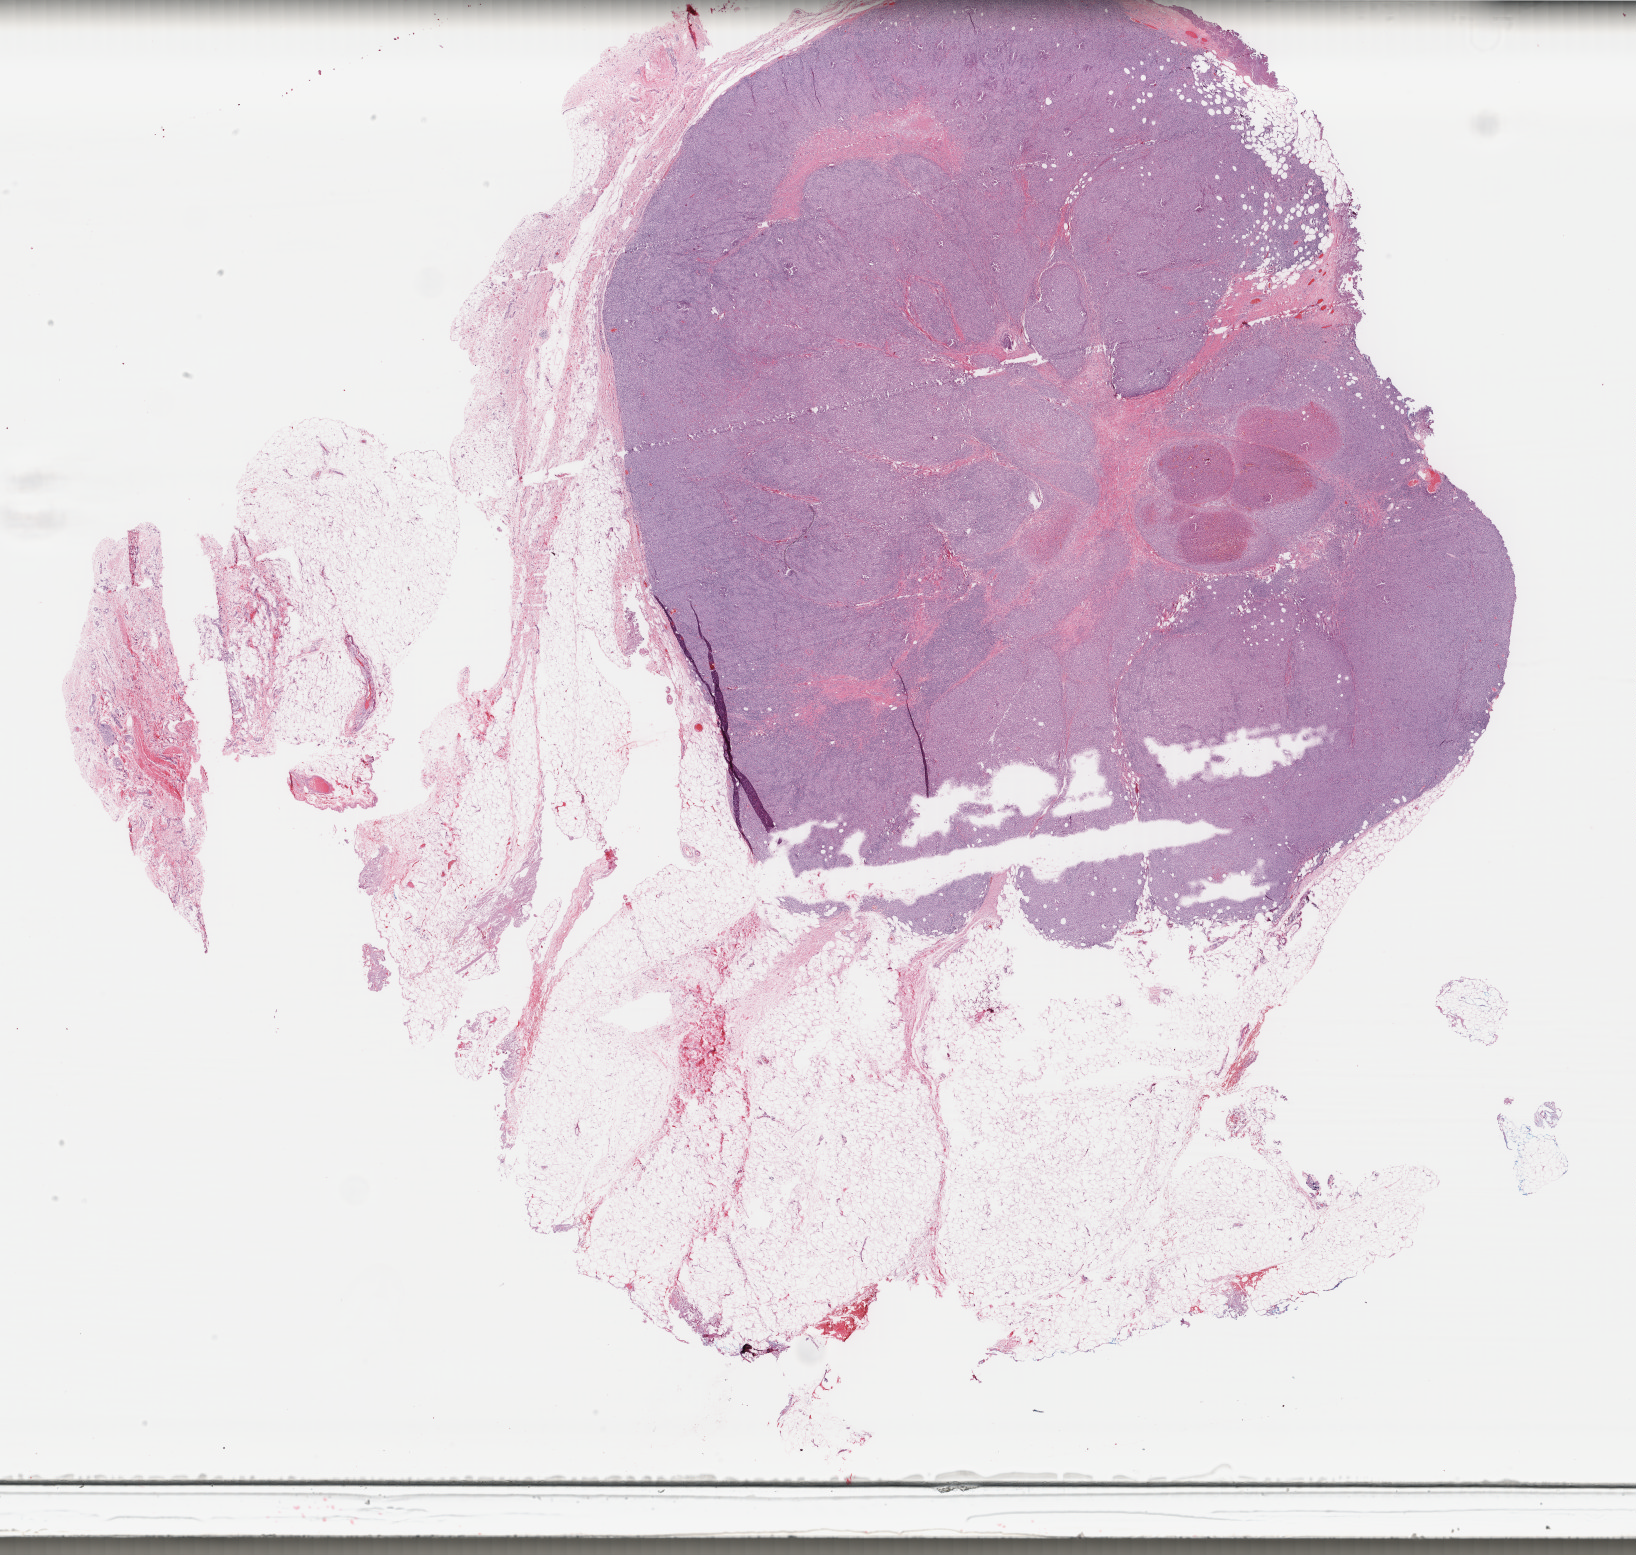
Hematoxylin and eosin (H&E) stained whole-slide image, whole scanned area (about 26.0 x 24.7 mm, acquisition: 40x scan) shown as a low-resolution overview. Formalin-fixed paraffin-embedded (FFPE) diagnostic section. Skin, primary tumour sample. Female patient; age at initial diagnosis 48 years.
Diagnosis: Malignant melanoma, NOS.